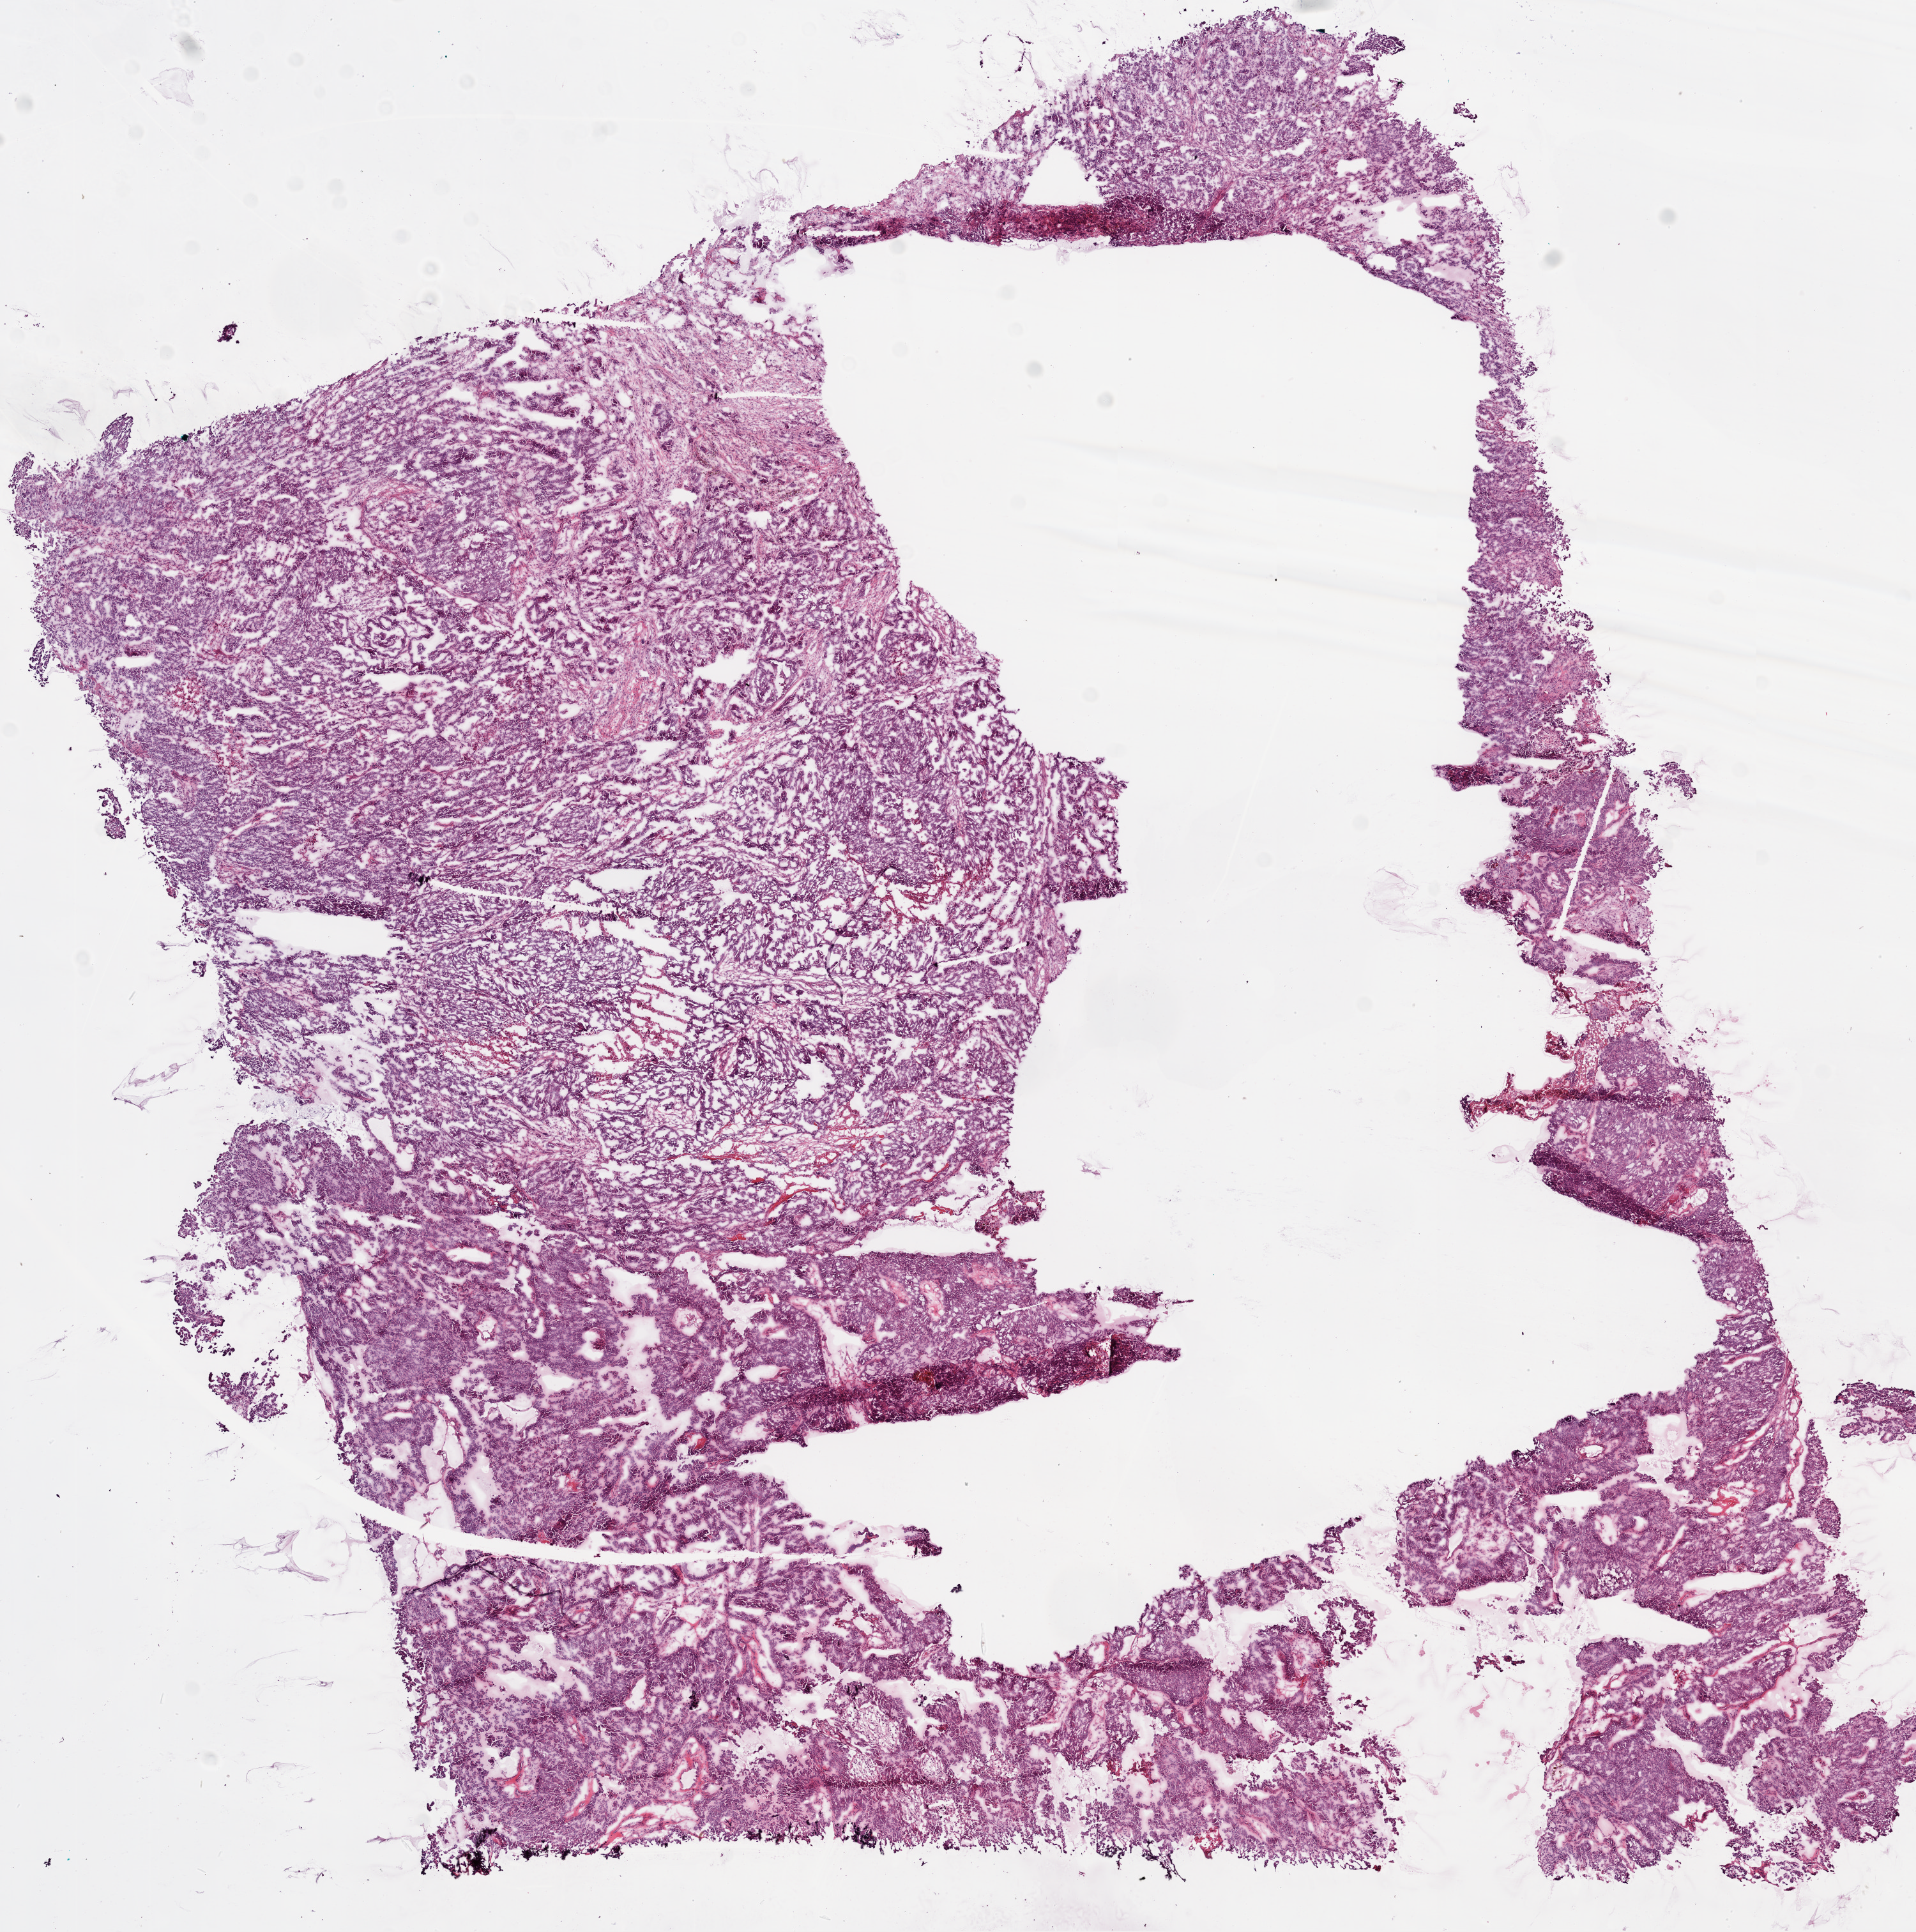
H&E whole-slide image — shown as a low-resolution overview of the whole scanned area (about 12.0 x 12.1 mm); frozen section from the bottom of the tissue portion; ovary, primary tumour sample. Patient: female, age at initial diagnosis 48 years.
Pathologic diagnosis: Serous cystadenocarcinoma, NOS.